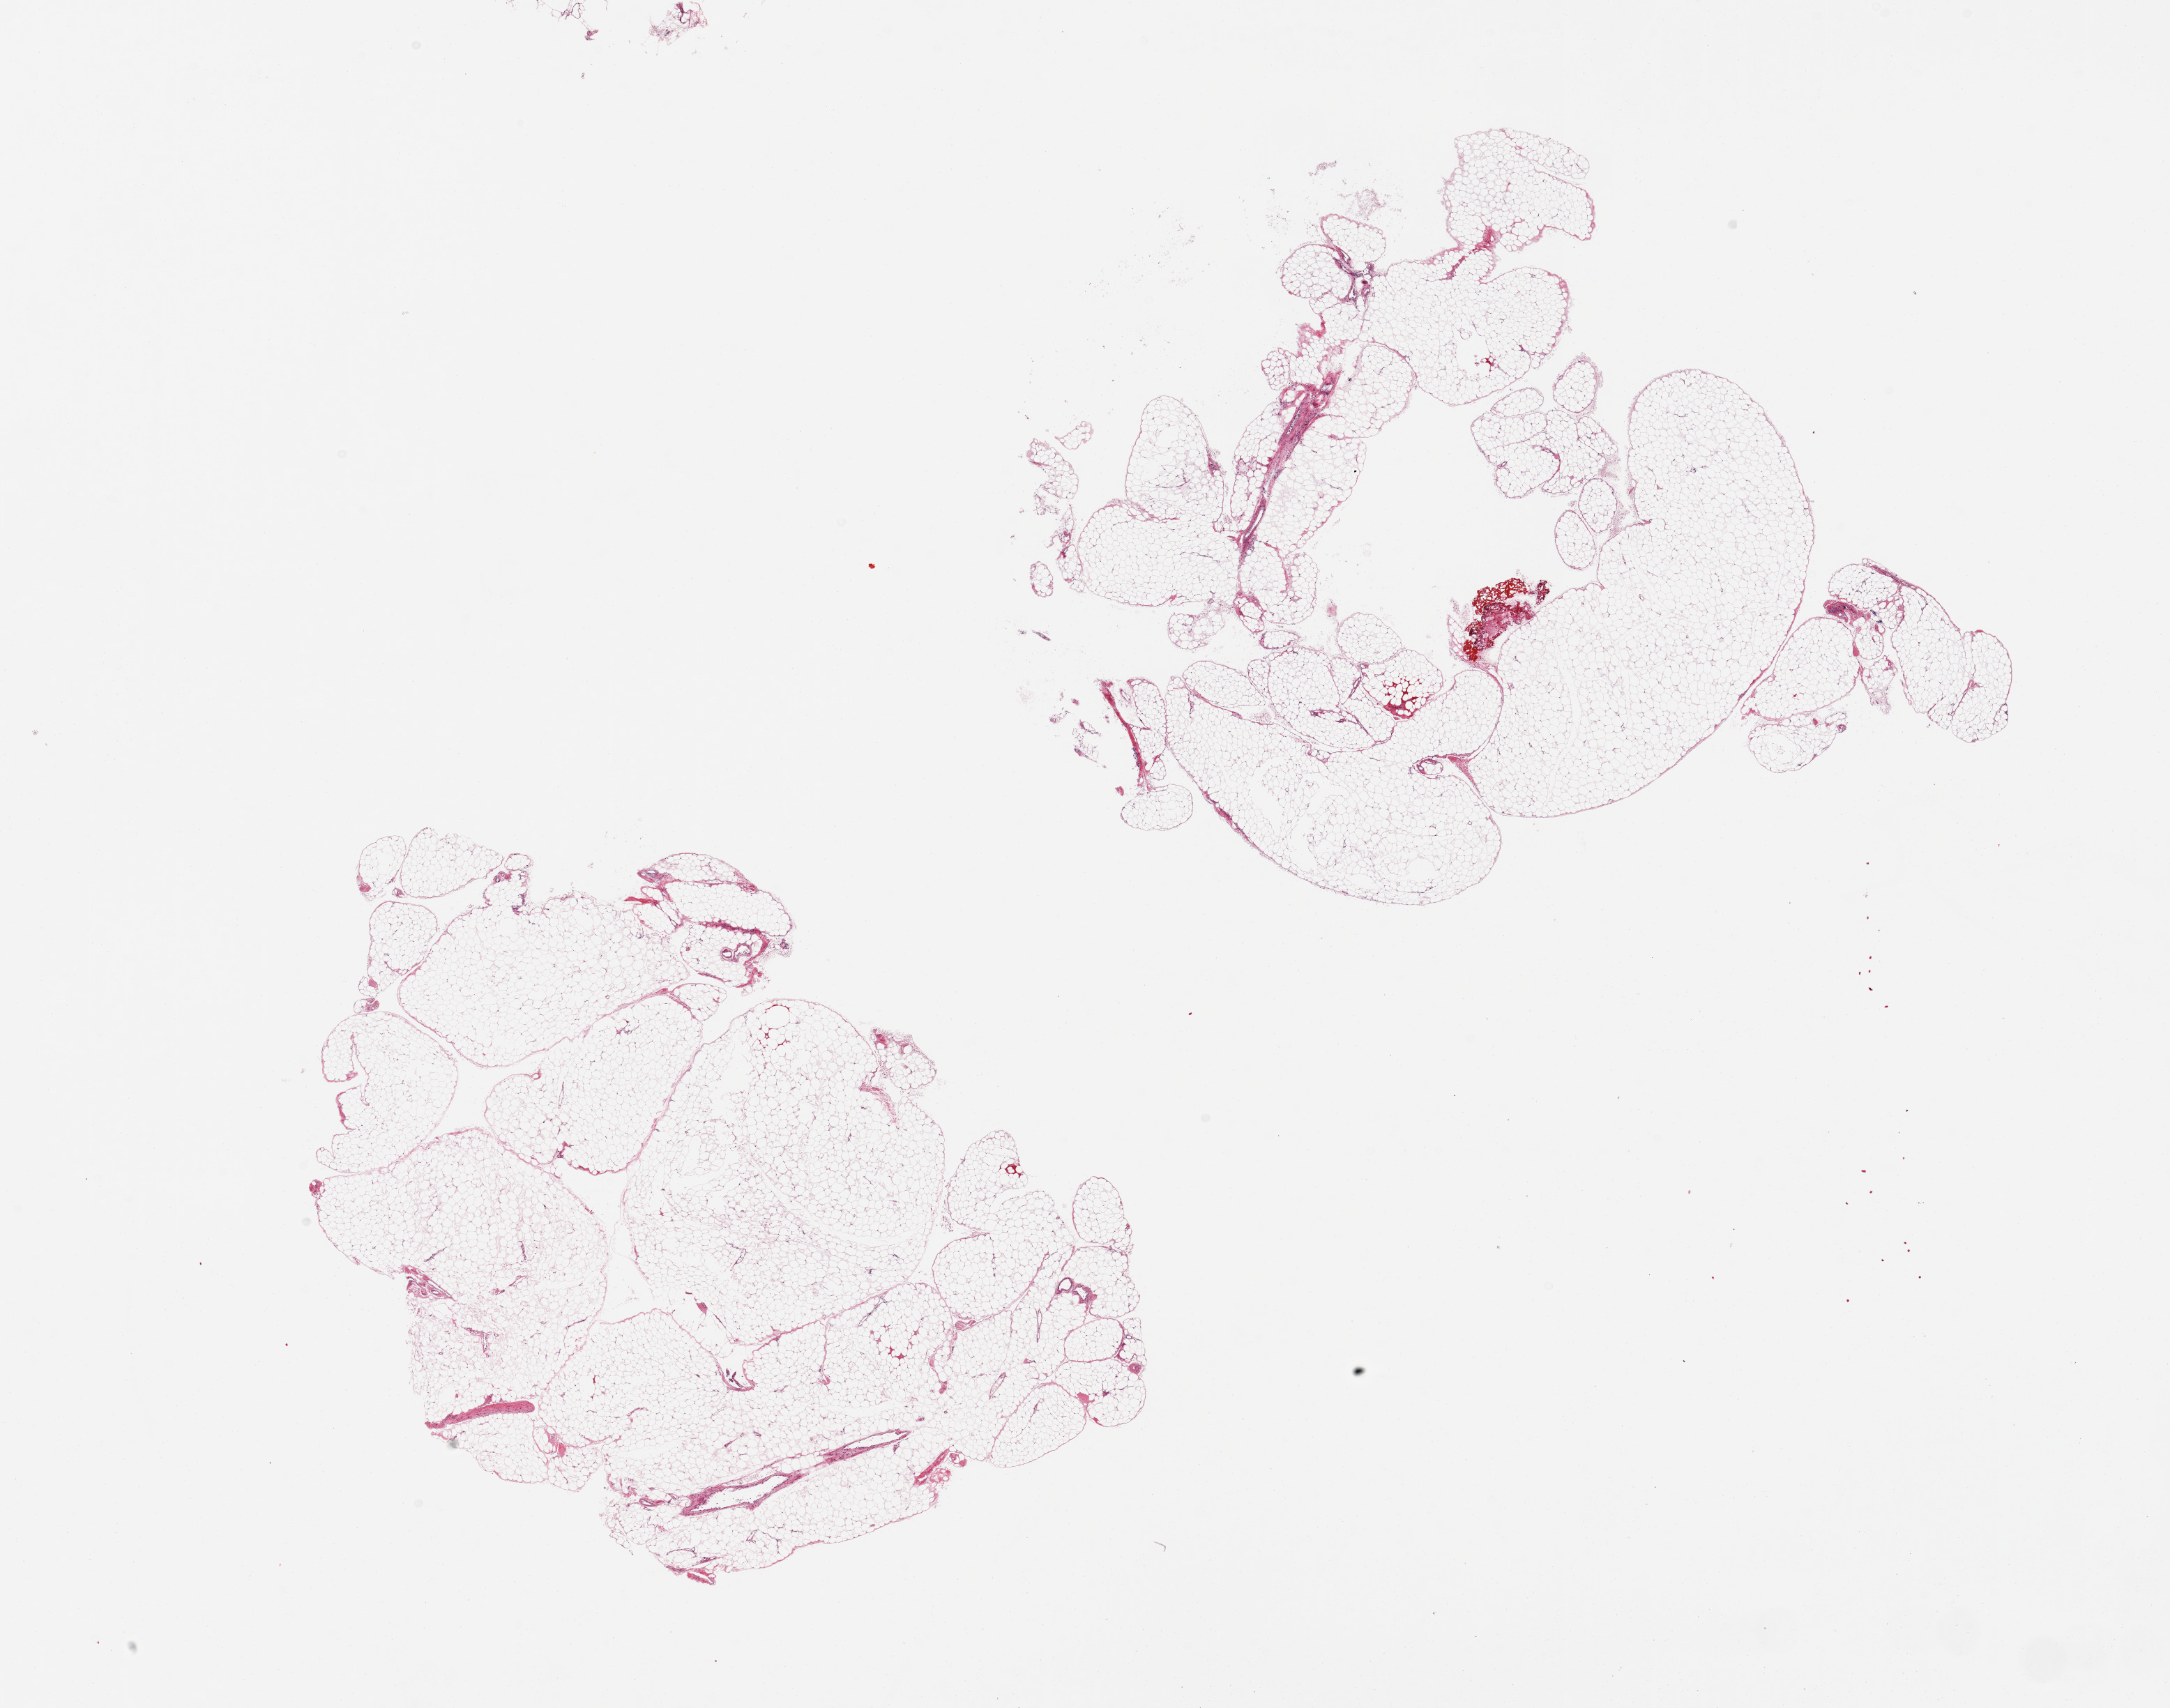
Whole-slide image, H&E stain — whole scanned area (about 24.6 x 19.4 mm, acquisition: 20x scan) shown as a low-resolution overview; PAXgene-fixed paraffin-embedded (PFPE) section; target tissue: omentum; tissue donor sample. Donor sex: female.
Reviewer comment on this tissue sample: 2 pieces, a few vessels.